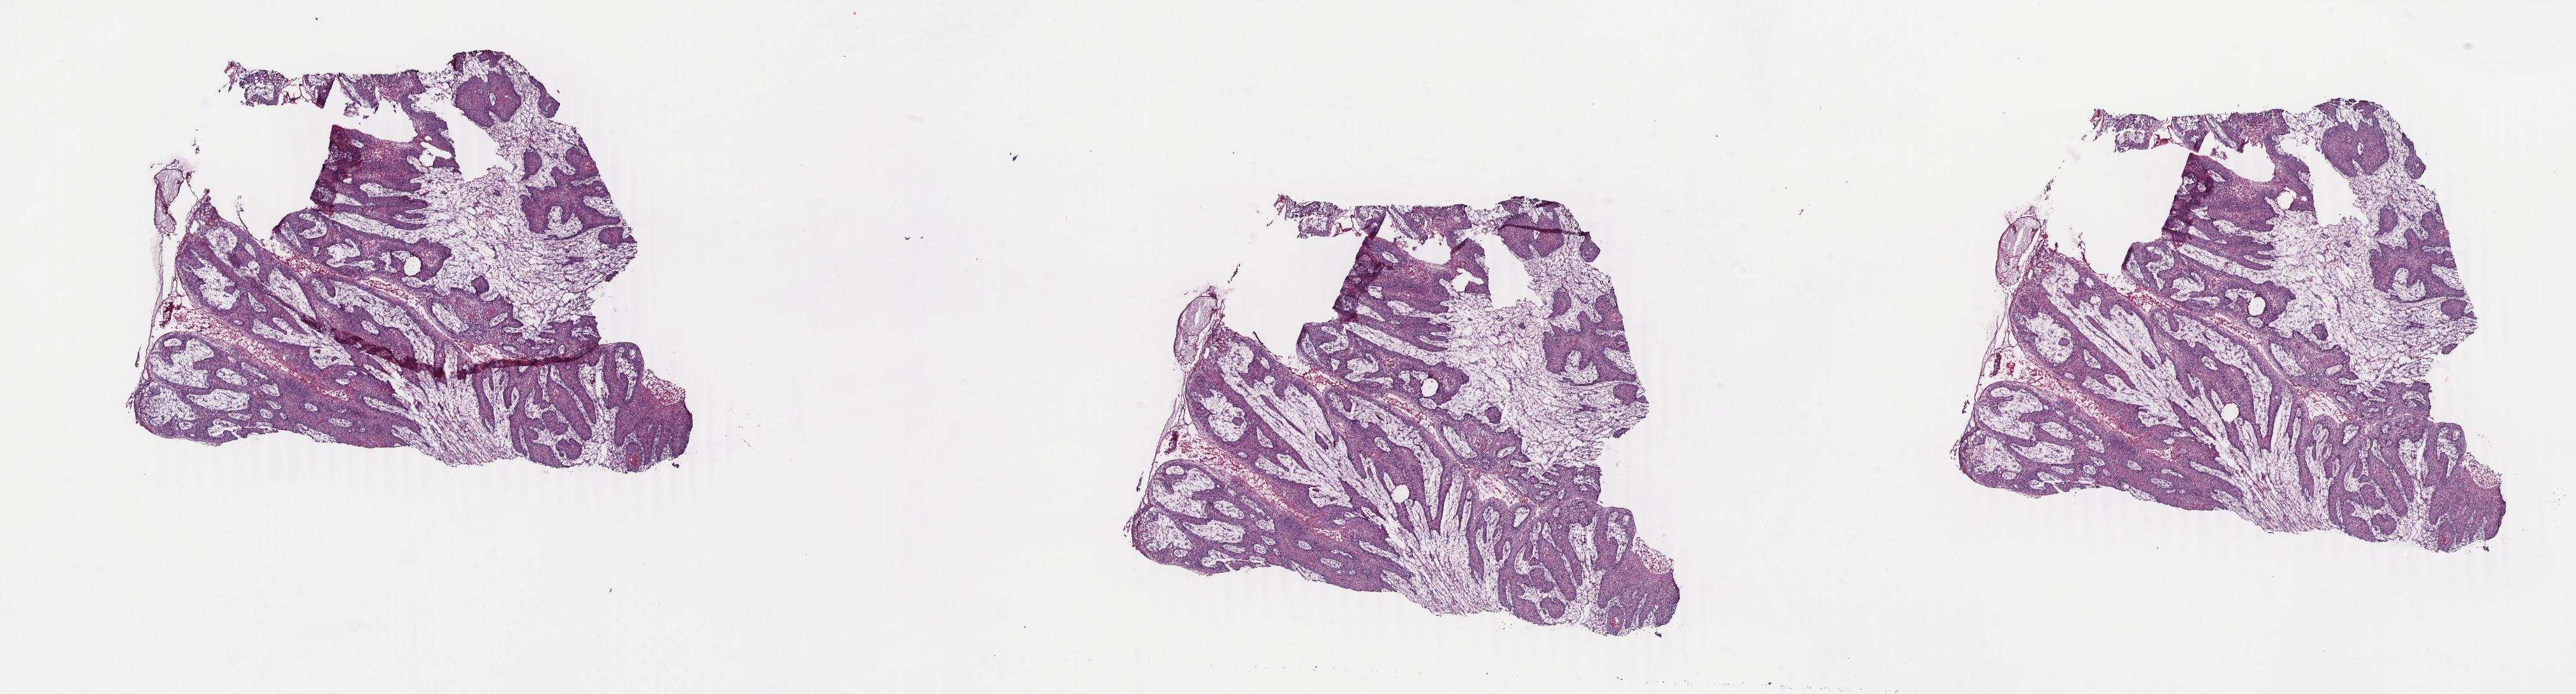
Hematoxylin and eosin (H&E) stained whole-slide image, a low-resolution overview of the entire scanned area, about 32.1 x 8.7 mm, frozen section from the top of the tissue portion, head and neck, primary tumour sample. Patient: female, age at initial diagnosis 41 years. Histologic grade: G1 (well differentiated). Pathologist review of this section (percent, as recorded): tumour cells 30%, tumour nuclei 75%, normal cells 0%, stromal cells 60%, necrosis 10%. Infiltration values recorded for this section: lymphocyte infiltration 4%, monocyte infiltration 1%, neutrophil infiltration 1%.
- diagnosis: Squamous cell carcinoma, NOS (cheek mucosa)
- AJCC pathologic stage: IVA (7th edition)
- TNM: T4a N2b MX